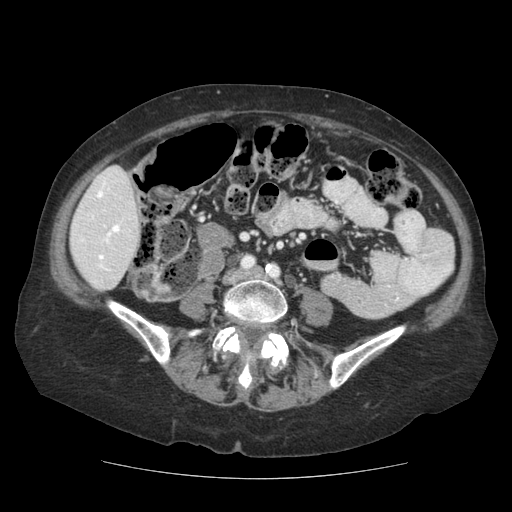
Contrast-enhanced abdominal CT (liver protocol), one axial slice. Slice 28 of 111 in the series (ordered by position). Soft-tissue window (W 400 / L 40 HU). 512 × 512 image matrix, field of view 360 × 360 mm. Case-level facts recorded for this patient, not image findings: diagnosis: hepatocellular carcinoma (patient treated with transarterial chemoembolisation; whether this scan precedes or follows treatment is not stated here); TNM stage (as recorded): Stage-I; Child-Pugh class: A.
Structures marked on this image (semi-automatic segmentation, software-assisted and operator-edited):
- liver parenchyma outside the tumour (the mass and vessels are separate outlines, so this box may not span the whole liver): bounding box [x1, y1, x2, y2] px = [70, 166, 140, 290]
- liver vessels: [81, 180, 120, 271]